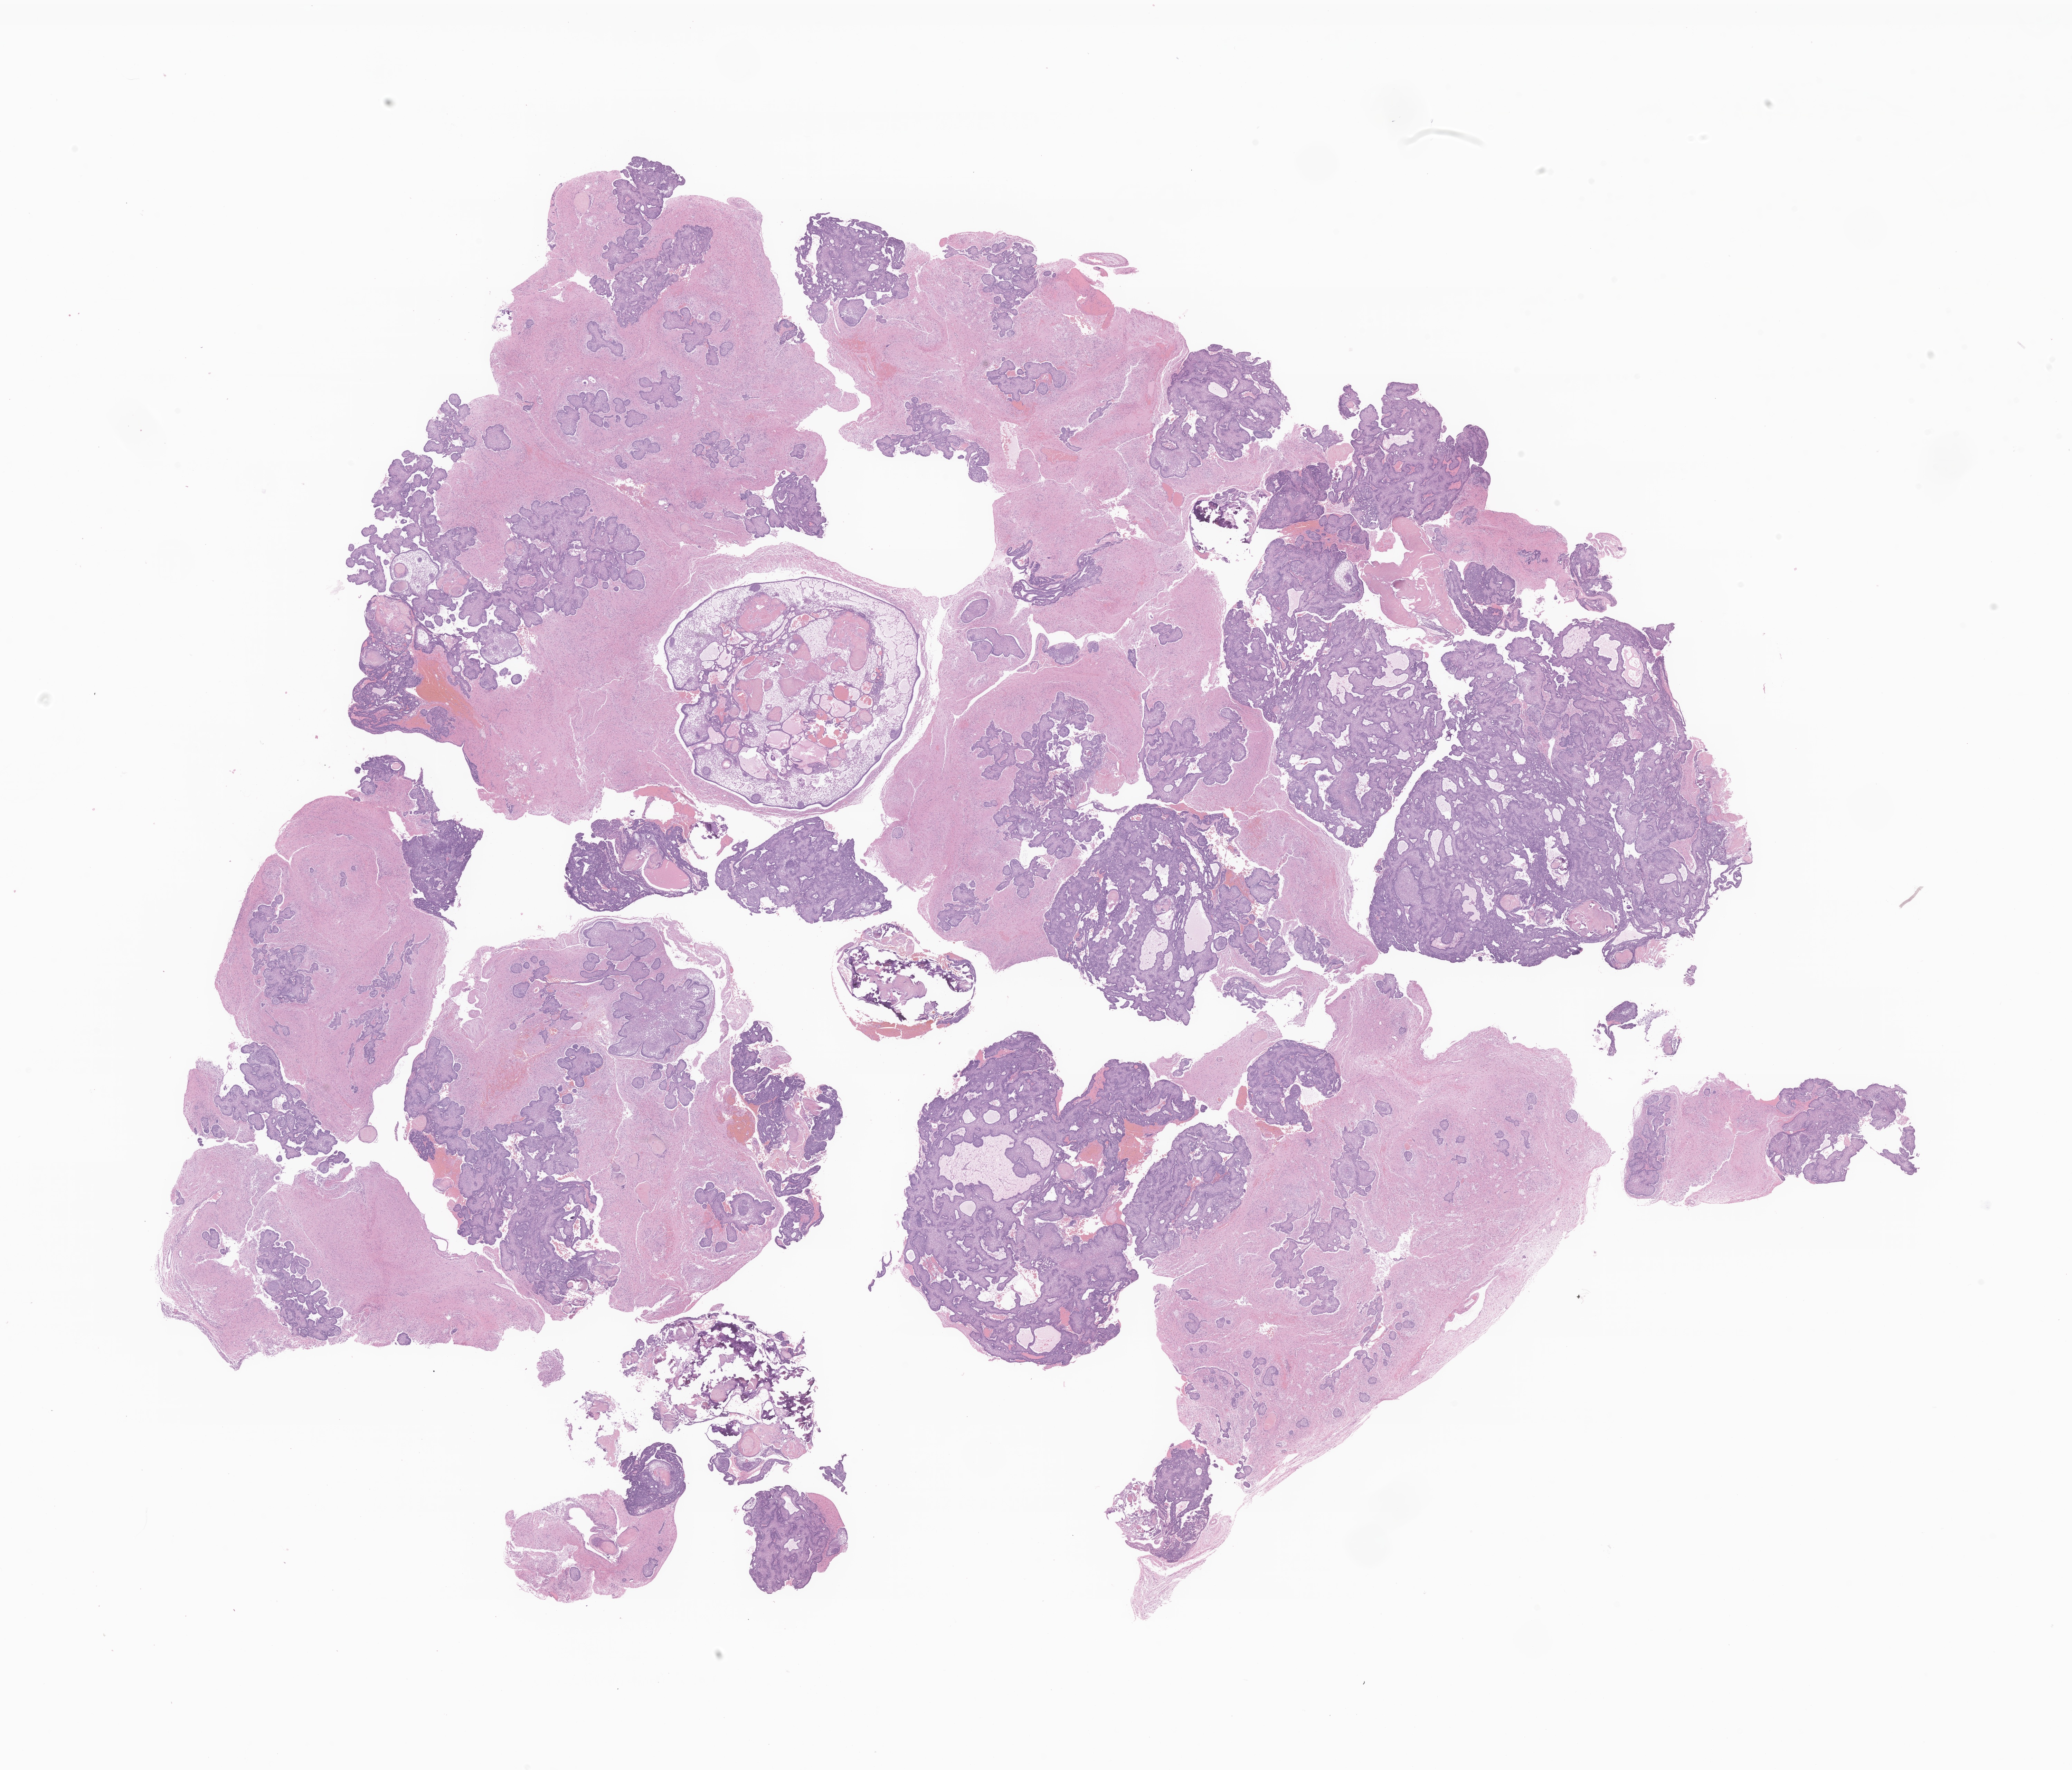
H&E whole-slide image of tumor tissue from the brain — low-resolution overview of the scanned area, about 25.3 x 21.6 mm, FFPE section. Patient female; age 82 months.
Diagnosis: Craniopharyngioma, adamantinomatous.